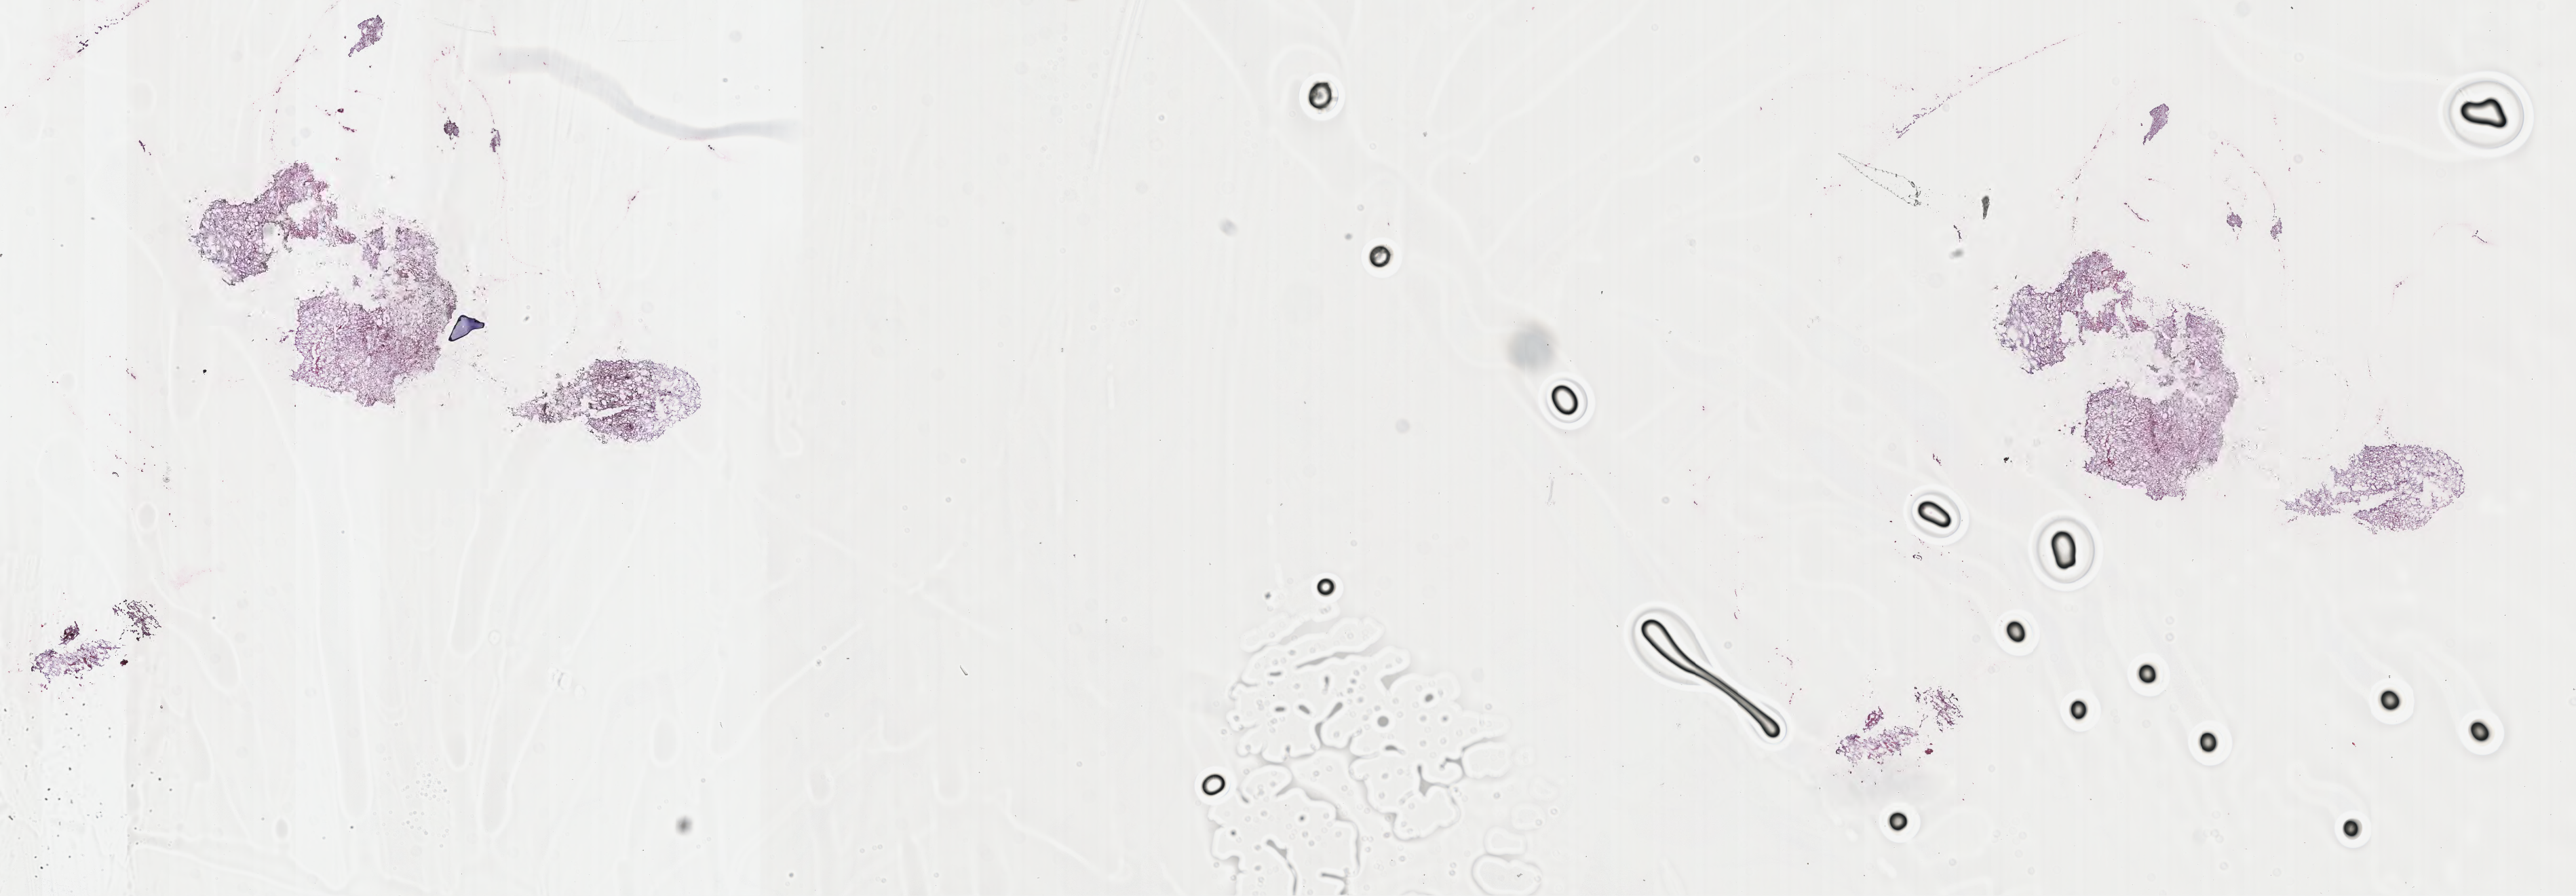
Haematoxylin and eosin whole-slide image of tumor tissue from the brain — whole scanned area (about 30.7 x 10.7 mm) shown as a low-resolution overview. Frozen section (OCT-embedded). Patient male; age 182 months (15 years 2 months).
Recorded diagnosis: Astrocytoma, NOS.